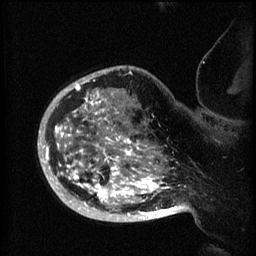
Breast MRI (dynamic contrast-enhanced), one sagittal slice; slice 49 of 60 in the series (ordered by position); 3 images stored at this slice position (order not interpretable as contrast timing); 1.5 T; TE 4.2 ms, TR 8.2 ms; 256 × 256 image matrix, field of view 200 × 200 mm. Patient: female, 50 years.
Annotated regions visible in this slice (semi-automatic segmentation, software-assisted and operator-edited):
- analysis volume of interest (the breast-tissue region the enhancement analysis was run in; not a lesion): bounding box <44,72,173,219> (left, top, right, bottom; pixels)
- tumour enhancement mask (voxels above the 70 % enhancement threshold inside the analysis volume of interest): <44,72,173,219>